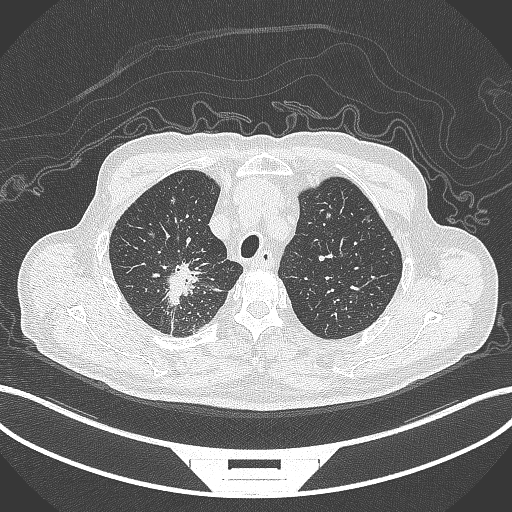
Chest CT, one axial slice. Position 306 of 407 along the scan axis. Reconstruction kernel B70f. 120 kVp. Lung window (W 1500 / L -600 HU). 1 mm slice thickness. 512 × 512 image matrix. Patient: male, 69 years. Case-level facts recorded for this patient, not image findings: clinical TNM (as recorded): T1c N1 M1.
Outlined on this slice (bounding box drawn by a radiologist):
- lung tumour (recorded histology: adenocarcinoma): bounding box (x1, y1, x2, y2) in pixels: (163, 263, 209, 313)